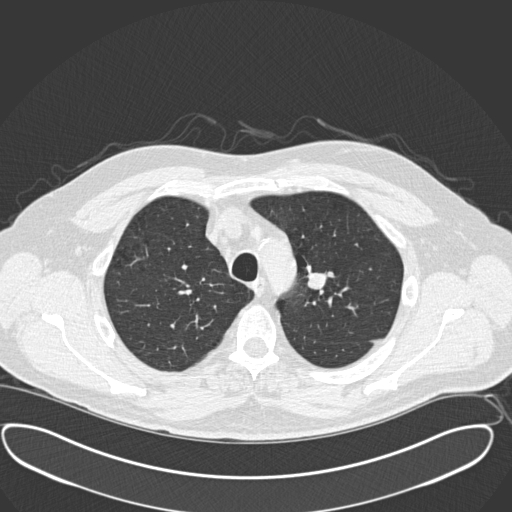
Axial slice from a low-dose chest CT screening exam. Third screening round (two years after baseline). Lung window (W 1500 / L -600 HU). 2 mm slice thickness. 120 kVp. Slice 43 of 181 in the series. 512 × 512 image matrix. Male, age 56 years at enrolment.
Expert reader's lesion annotation, box from (x=290, y=262) to (x=343, y=309) px. Screening reader's record for this exam: no non-calcified nodule ≥4 mm recorded. Lung cancer was diagnosed 156 days after this screen: neuroendocrine carcinoma, NOS, left upper lobe, well differentiated (G1), stage IA (AJCC 6th edition), 20 mm at pathology.